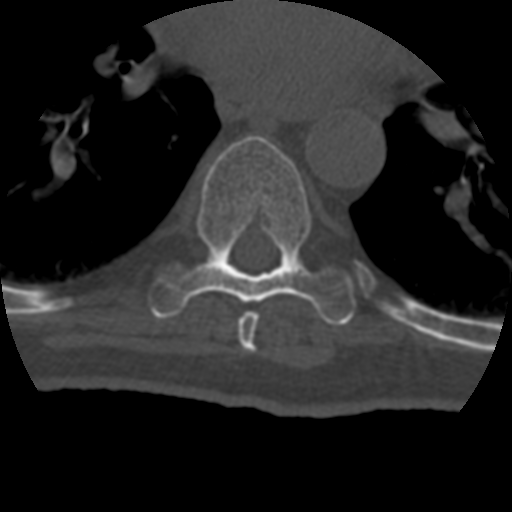
CT including the spine, one axial slice; position 262 of 399 along the scan axis; reconstruction kernel STANDARD; bone window (W 1800 / L 400 HU); 1.25 mm slice thickness; 512 × 512 image matrix, field of view 160 × 160 mm. Patient age 69 years. Case-level facts recorded for this patient, not image findings: primary cancer: prostate.
Annotated regions visible in this slice (semi-automatic segmentation, software-assisted and operator-edited):
- T7 vertebra: bounding box [x1, y1, x2, y2] px = [238, 311, 259, 353]
- T8 vertebra: [149, 135, 355, 325]